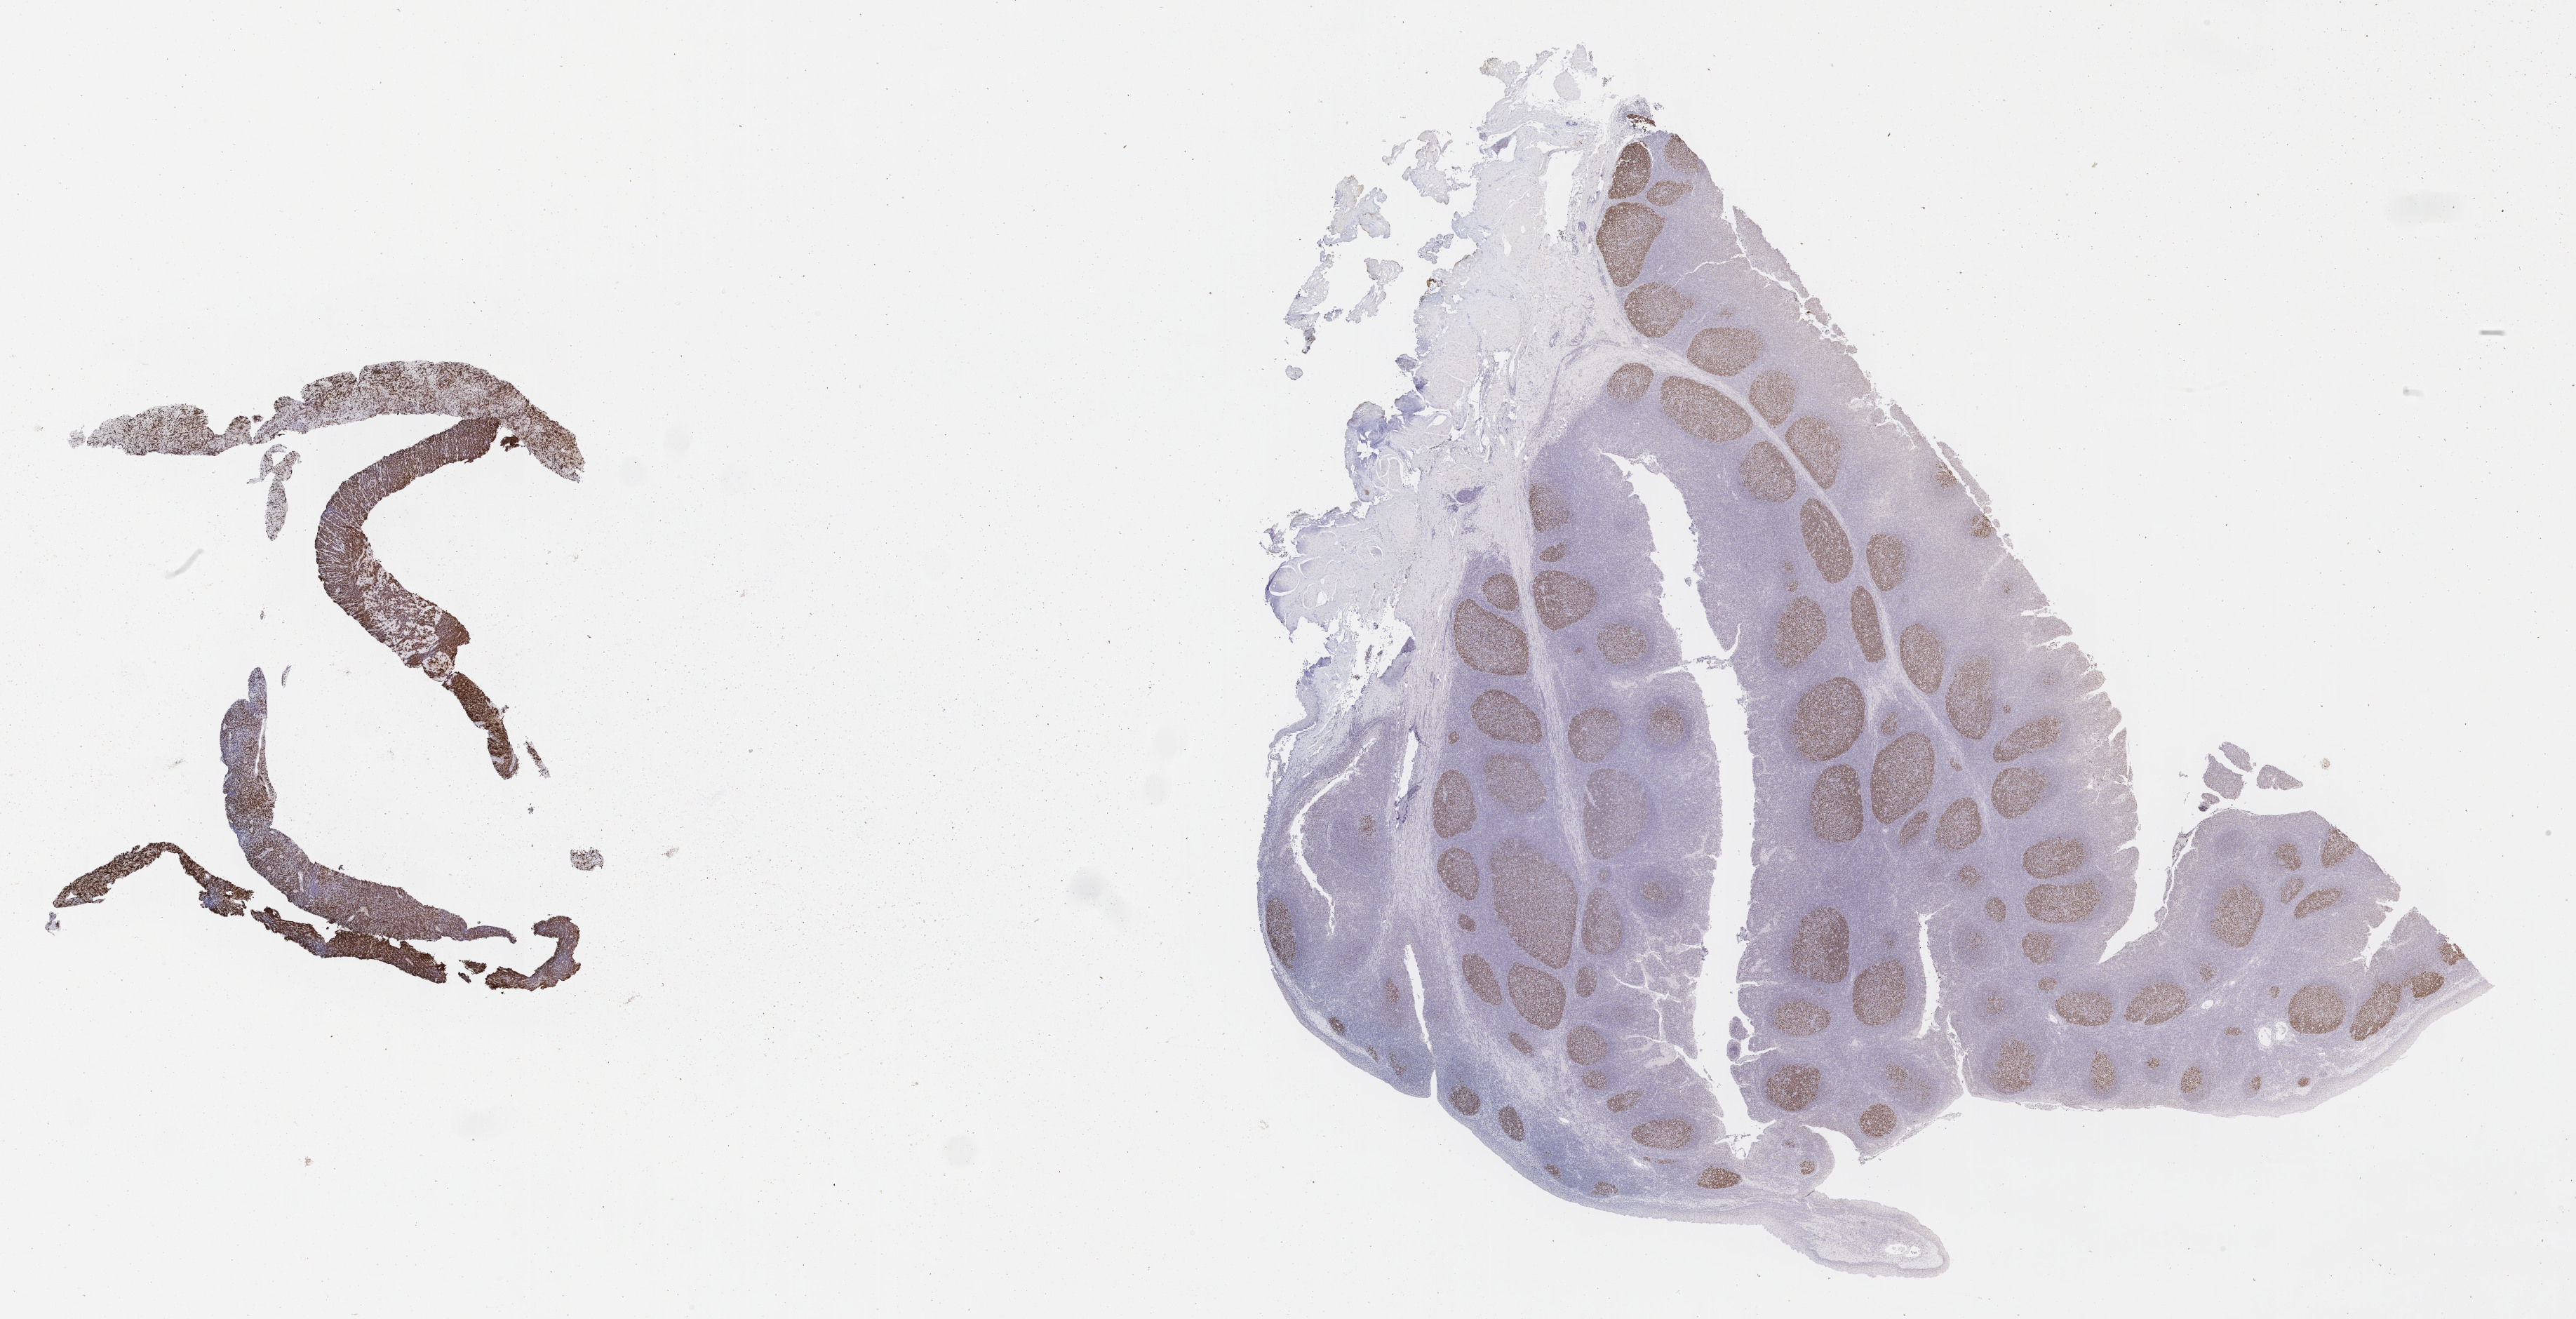
Whole-slide image, immunohistochemical stain for BCL6 — whole scanned area (about 29.7 x 15.2 mm) shown as a low-resolution overview; tumor tissue; anatomic site: pleura. Male patient; age at initial diagnosis 2 years.
Histologic diagnosis: Diffuse large B-cell lymphoma, NOS.